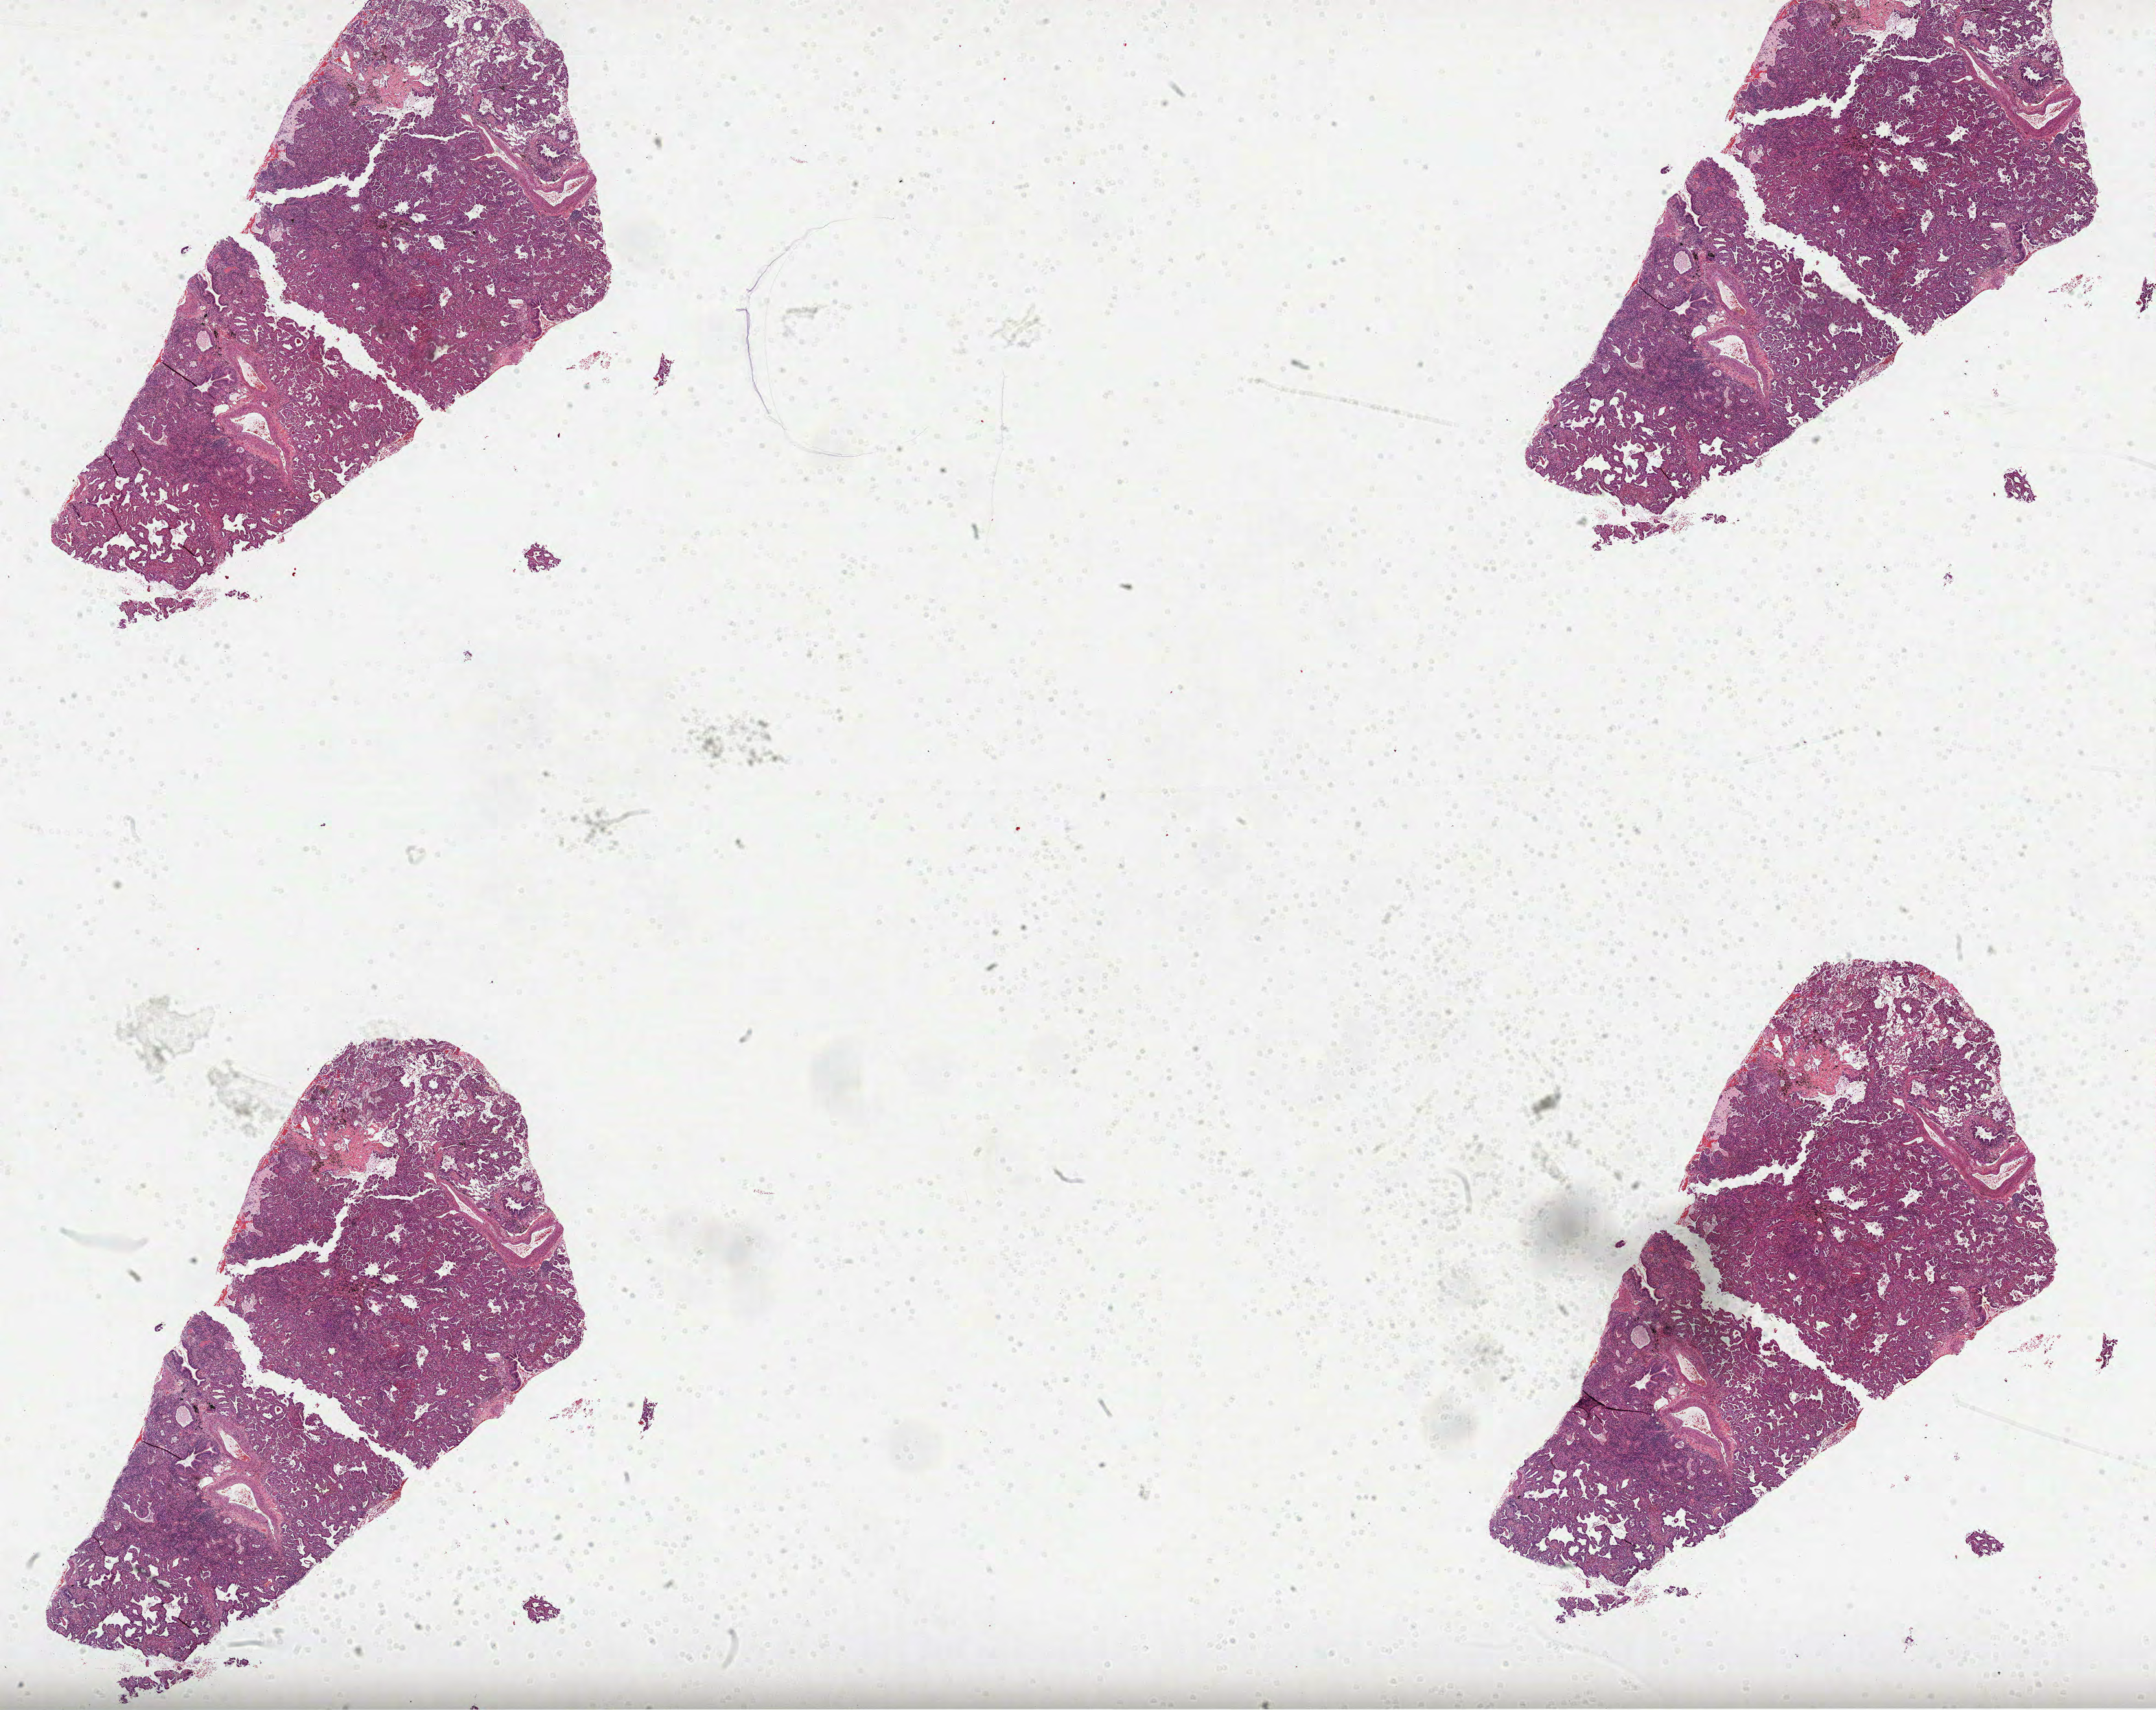
Whole-slide histology image, H&E-stained — low-resolution overview of the scanned area, about 26.8 x 21.3 mm (from a 40x scan); formalin-fixed paraffin-embedded (FFPE) diagnostic section; primary tumour sample from the lung. Male patient; age at initial diagnosis 43 years.
AJCC pathologic stage: IB (6th edition). Laterality: right. Pathologic diagnosis: Adenocarcinoma, NOS (upper lobe, lung).